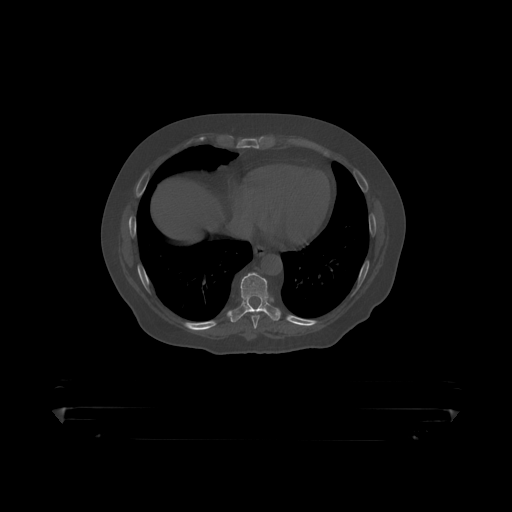
CT including the spine, one axial slice; position 242 of 390 along the scan axis; reconstruction kernel STANDARD; 120 kVp; bone window (W 1800 / L 400 HU); 512 × 512 image matrix, field of view 650 × 650 mm. Male patient, age 60 years. From the clinical record (not read from this slice): primary cancer: prostate.
Structures marked on this image (semi-automatically segmented with operator editing):
- T8 vertebra: bounding box [x1, y1, x2, y2] px = [252, 315, 260, 319]
- T9 vertebra: [230, 273, 281, 318]